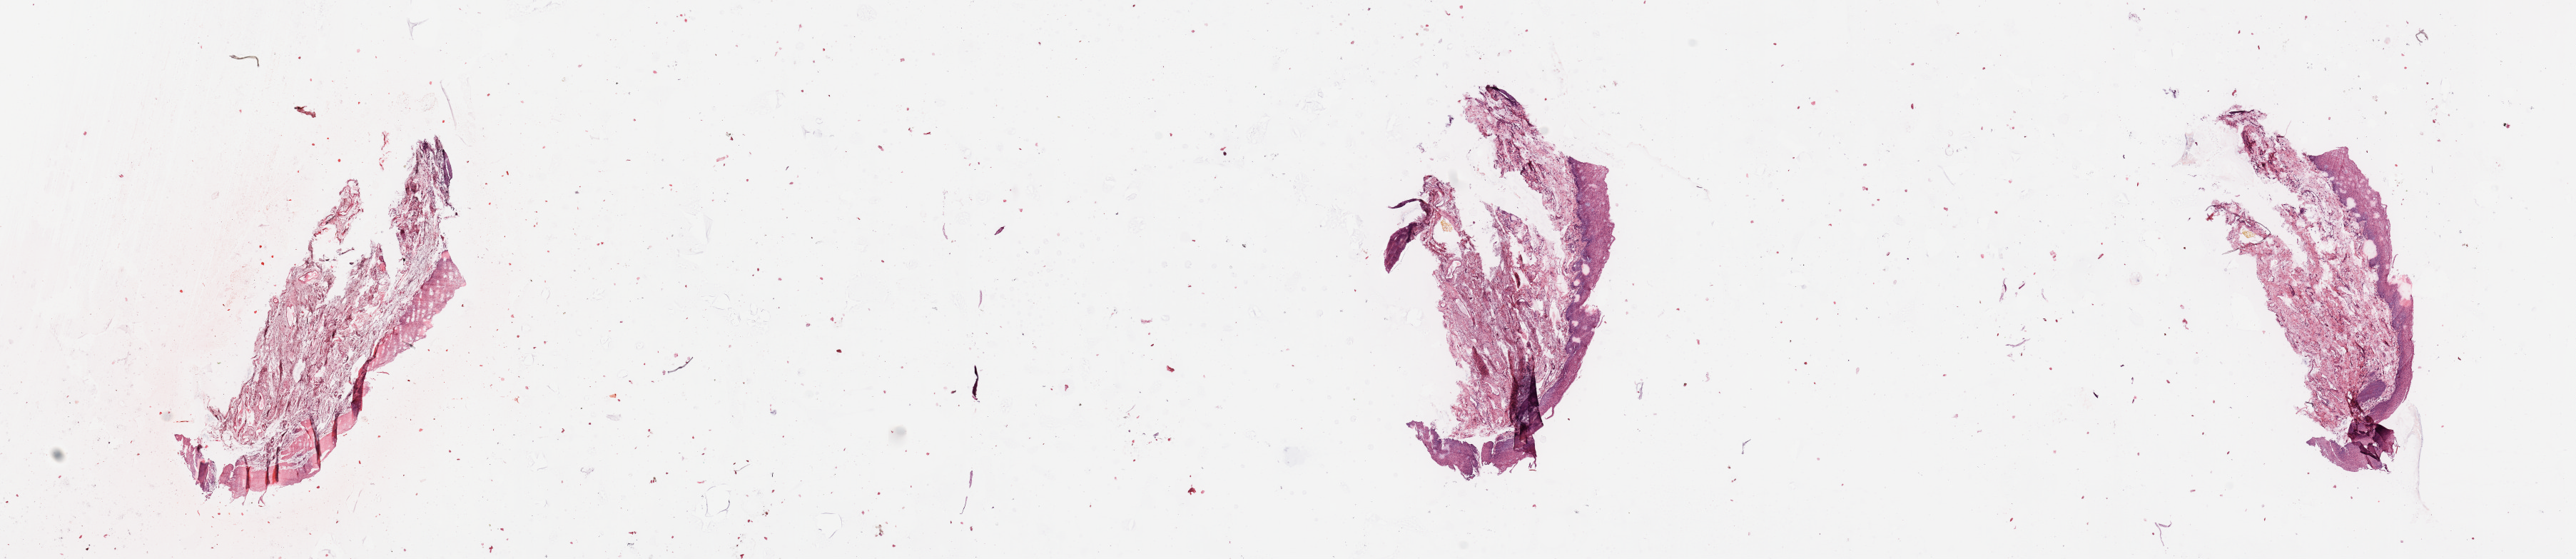
Hematoxylin and eosin (H&E) stained whole-slide image — low-resolution overview of the scanned area, about 28.5 x 6.2 mm (slide scanned at 20x); normal (non-tumour) tissue sample, sampled site: larynx. Patient: male, age 72 years.
This section: normal (non-tumour) tissue from the same patient. Patient diagnosis: Squamous cell carcinoma, NOS (larynx, NOS).